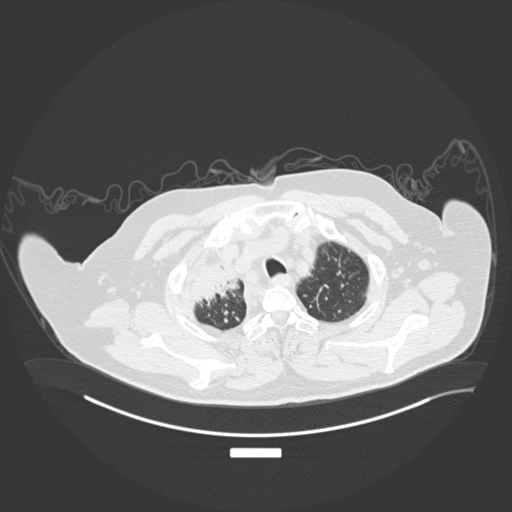
Chest CT, one axial slice. Slice 167 of 201 in the series (ordered by position). Reconstruction kernel B30f. 120 kVp. Lung window (W 1500 / L -600 HU). 1 mm slice thickness. 512 × 512 image matrix. Patient: male, 69 years. From the clinical record (not read from this slice): clinical TNM (as recorded): T4 N3 M1.
Outlined on this slice (rectangle marked by the reading radiologist):
- lung tumour (recorded histology: adenocarcinoma): bounding box <187,257,240,304> (left, top, right, bottom; pixels)